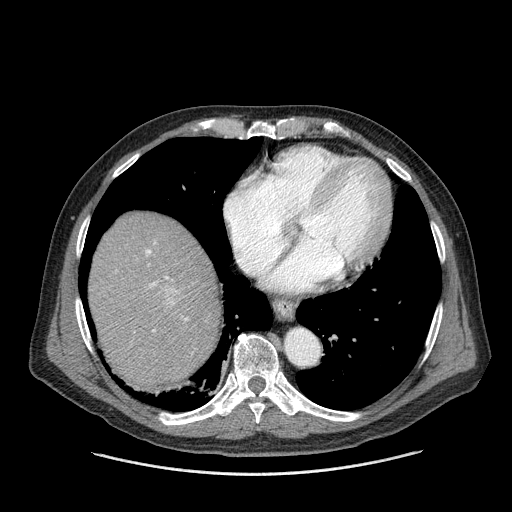
Contrast-enhanced abdominal CT (liver protocol), one axial slice; slice 140 of 180 in the series (ordered by position); one of 2 acquisitions stored at this slice position; soft-tissue window (W 400 / L 40 HU); 2.5 mm slice thickness; 512 × 512 image matrix, field of view 420 × 420 mm. Case-level facts recorded for this patient, not image findings: diagnosis: hepatocellular carcinoma (patient treated with transarterial chemoembolisation; whether this scan precedes or follows treatment is not stated here); TNM stage (as recorded): Stage-II; Child-Pugh class: A; tumour differentiation: well differentiated; tumour nodularity: multinodular.
Structures marked on this image (semi-automatic segmentation, software-assisted and operator-edited):
- abdominal aorta: bounding box (x1, y1, x2, y2) in pixels: (286, 330, 319, 364)
- liver parenchyma outside the tumour (the mass and vessels are separate outlines, so this box may not span the whole liver): (88, 212, 220, 390)
- mass: (159, 286, 184, 306)
- liver vessels: (145, 249, 188, 332)